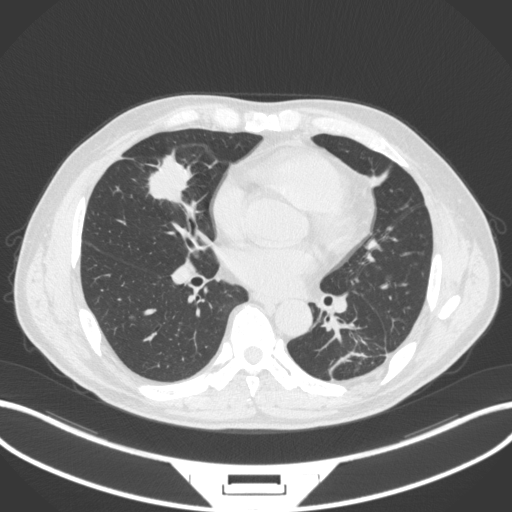
Chest CT, one axial slice; slice 136 of 399 in the series (ordered by position); 120 kVp; lung window (W 1500 / L -600 HU); 512 × 512 image matrix, field of view 400 × 400 mm. Patient: male, 59 years. From the clinical record (not read from this slice): clinical TNM (as recorded): T2a N1 M0.
Annotated regions visible in this slice (bounding box drawn by a radiologist):
- lung tumour (recorded histology: adenocarcinoma): bounding box [x1, y1, x2, y2] px = [143, 150, 201, 209]